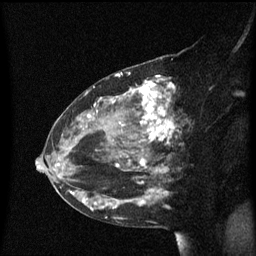
Breast MRI (dynamic contrast-enhanced), one sagittal slice. Position 34 of 60 along the scan axis. Dynamic contrast-enhanced series, image 2 of 3 at this slice position (ordered by acquisition). 1.5 T. TE 4.2 ms, TR 8.4 ms. 2 mm slice thickness. 256 × 256 image matrix, field of view 200 × 200 mm. Patient: female, 48 years. Case-level facts recorded for this patient, not image findings: setting: breast cancer imaged before/during neoadjuvant chemotherapy; receptor status: HR-positive, HER2-negative.
Outlined on this slice (semi-automatically segmented with operator editing):
- analysis volume of interest (the breast-tissue region the enhancement analysis was run in; not a lesion): bounding box [x1, y1, x2, y2] px = [80, 78, 189, 219]
- tumour enhancement mask (voxels above the 70 % enhancement threshold inside the analysis volume of interest): [90, 78, 177, 212]